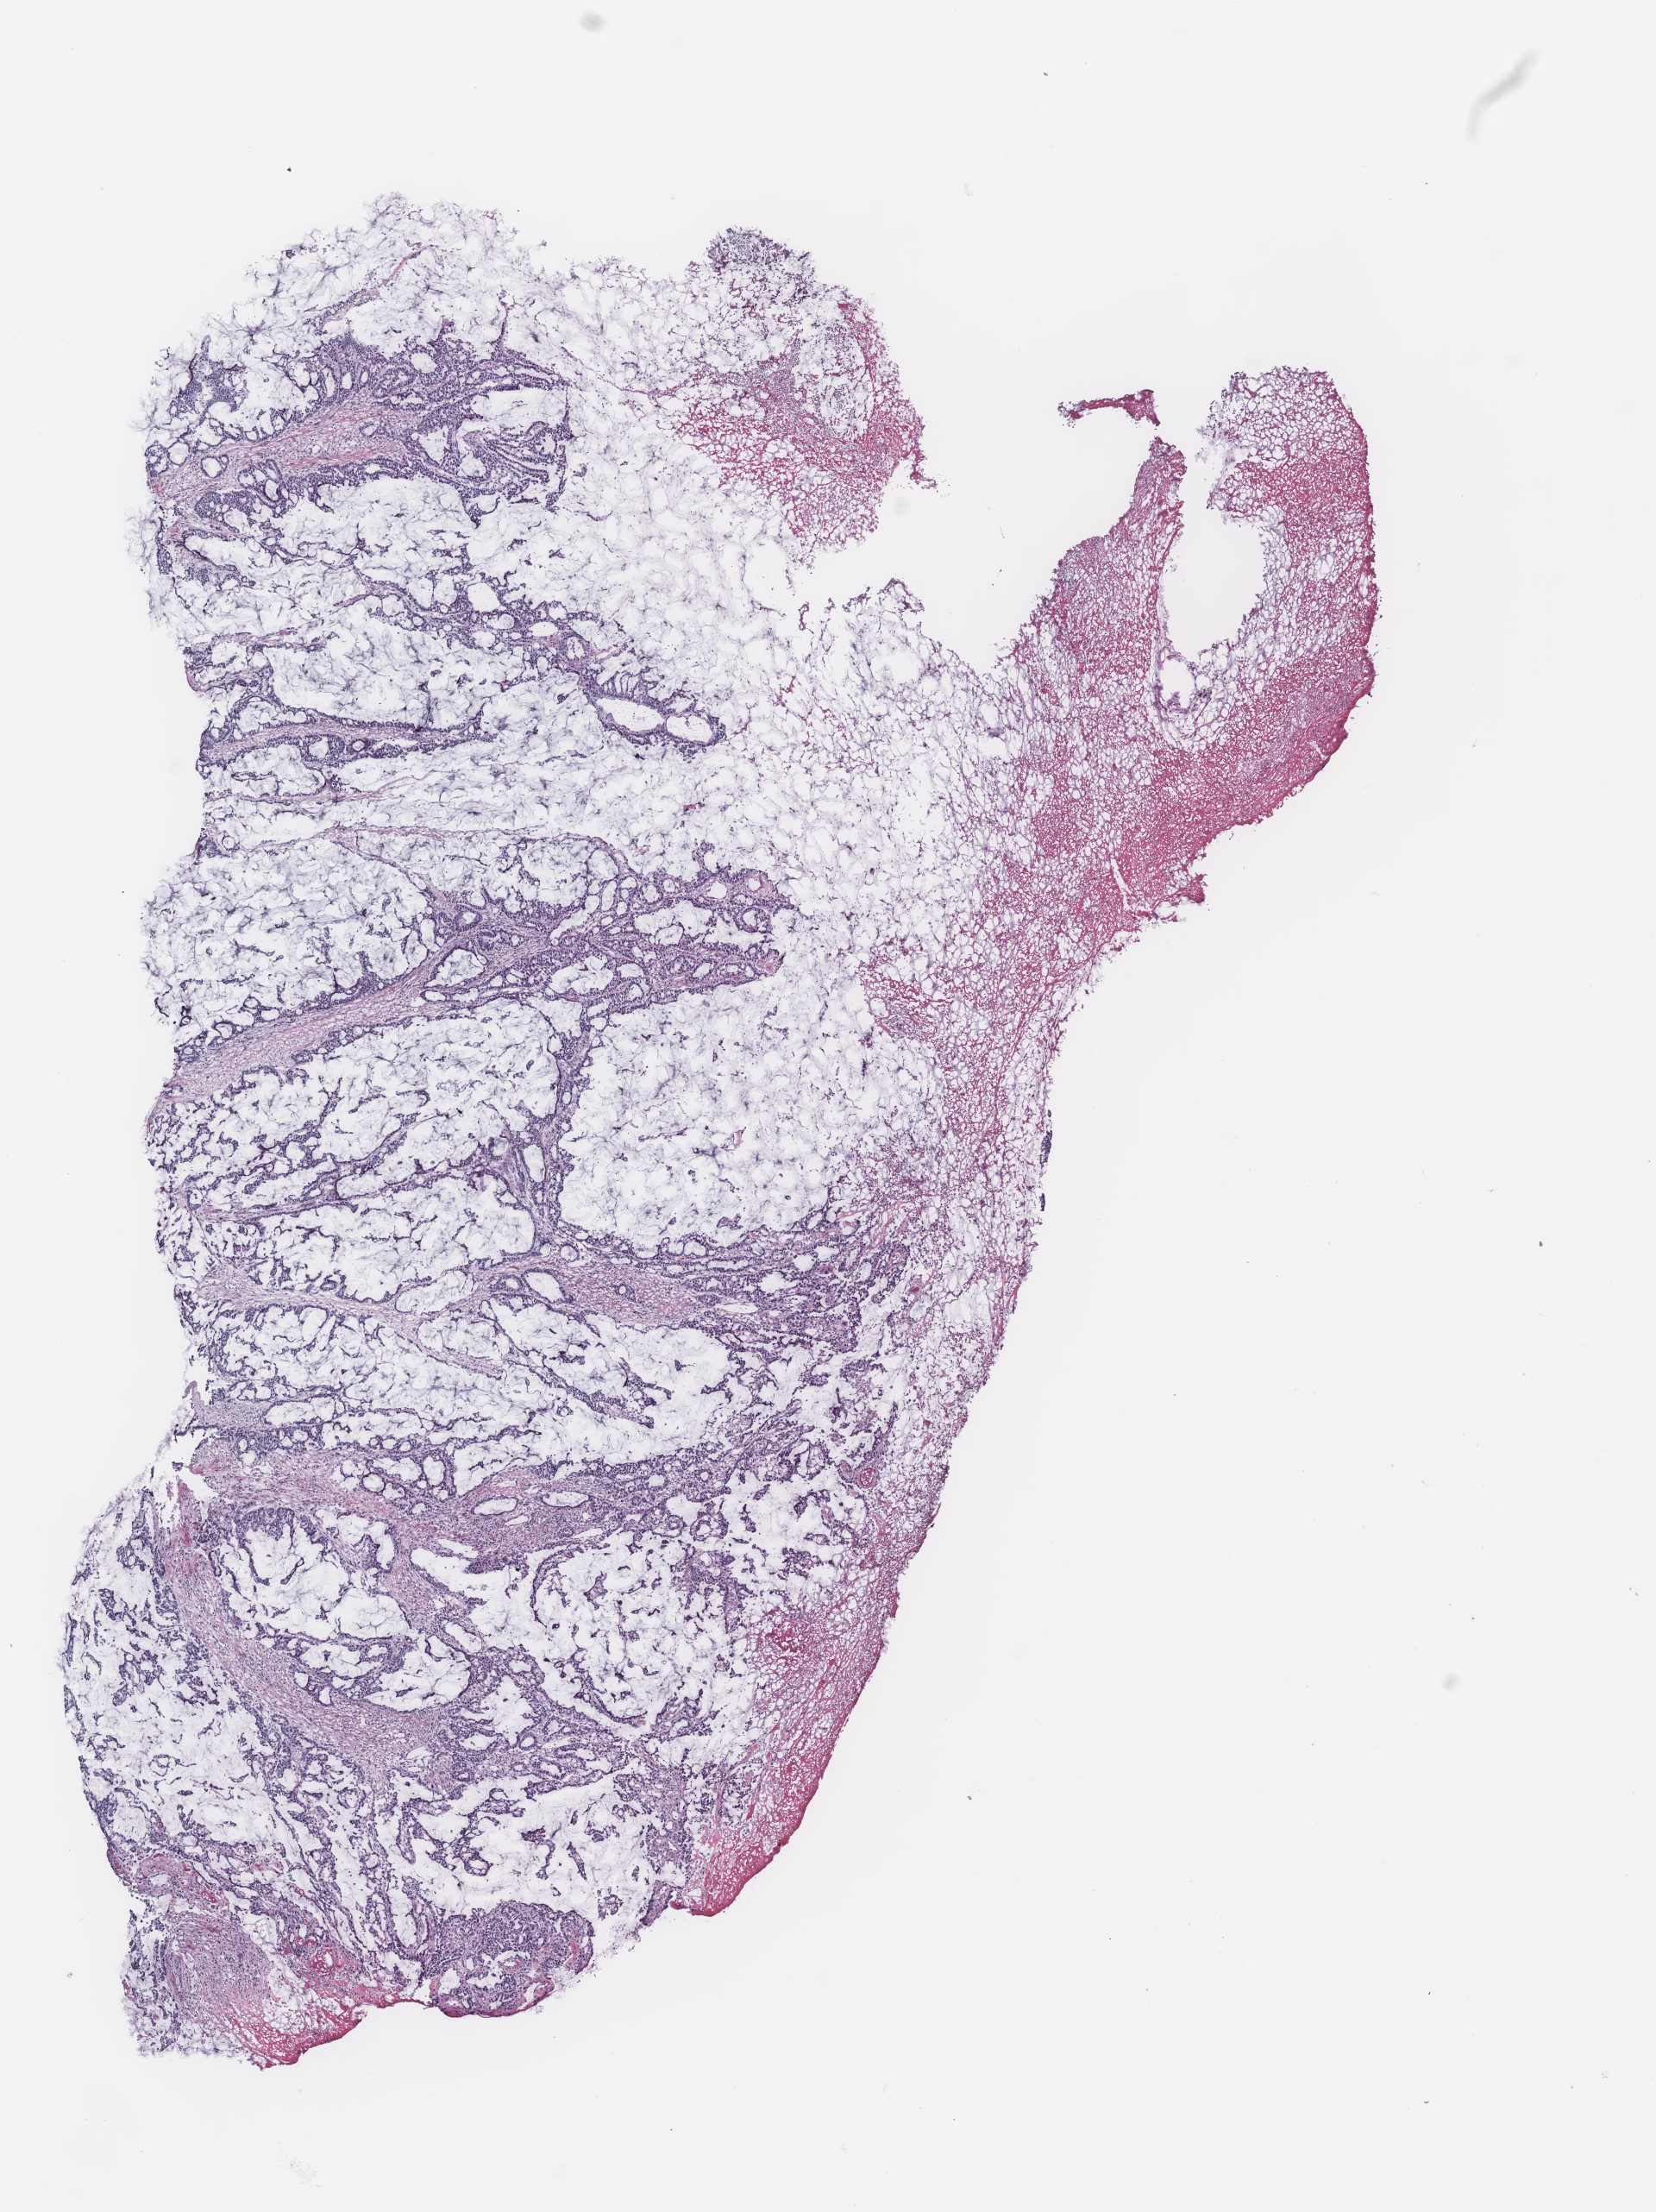
H&E-stained whole-slide image, whole scanned area (about 7.7 x 10.3 mm, slide scanned at 40x) shown as a low-resolution overview, colon, tissue type not recorded.
• patient diagnosis (cohort enrolment): colon cancer (colon)